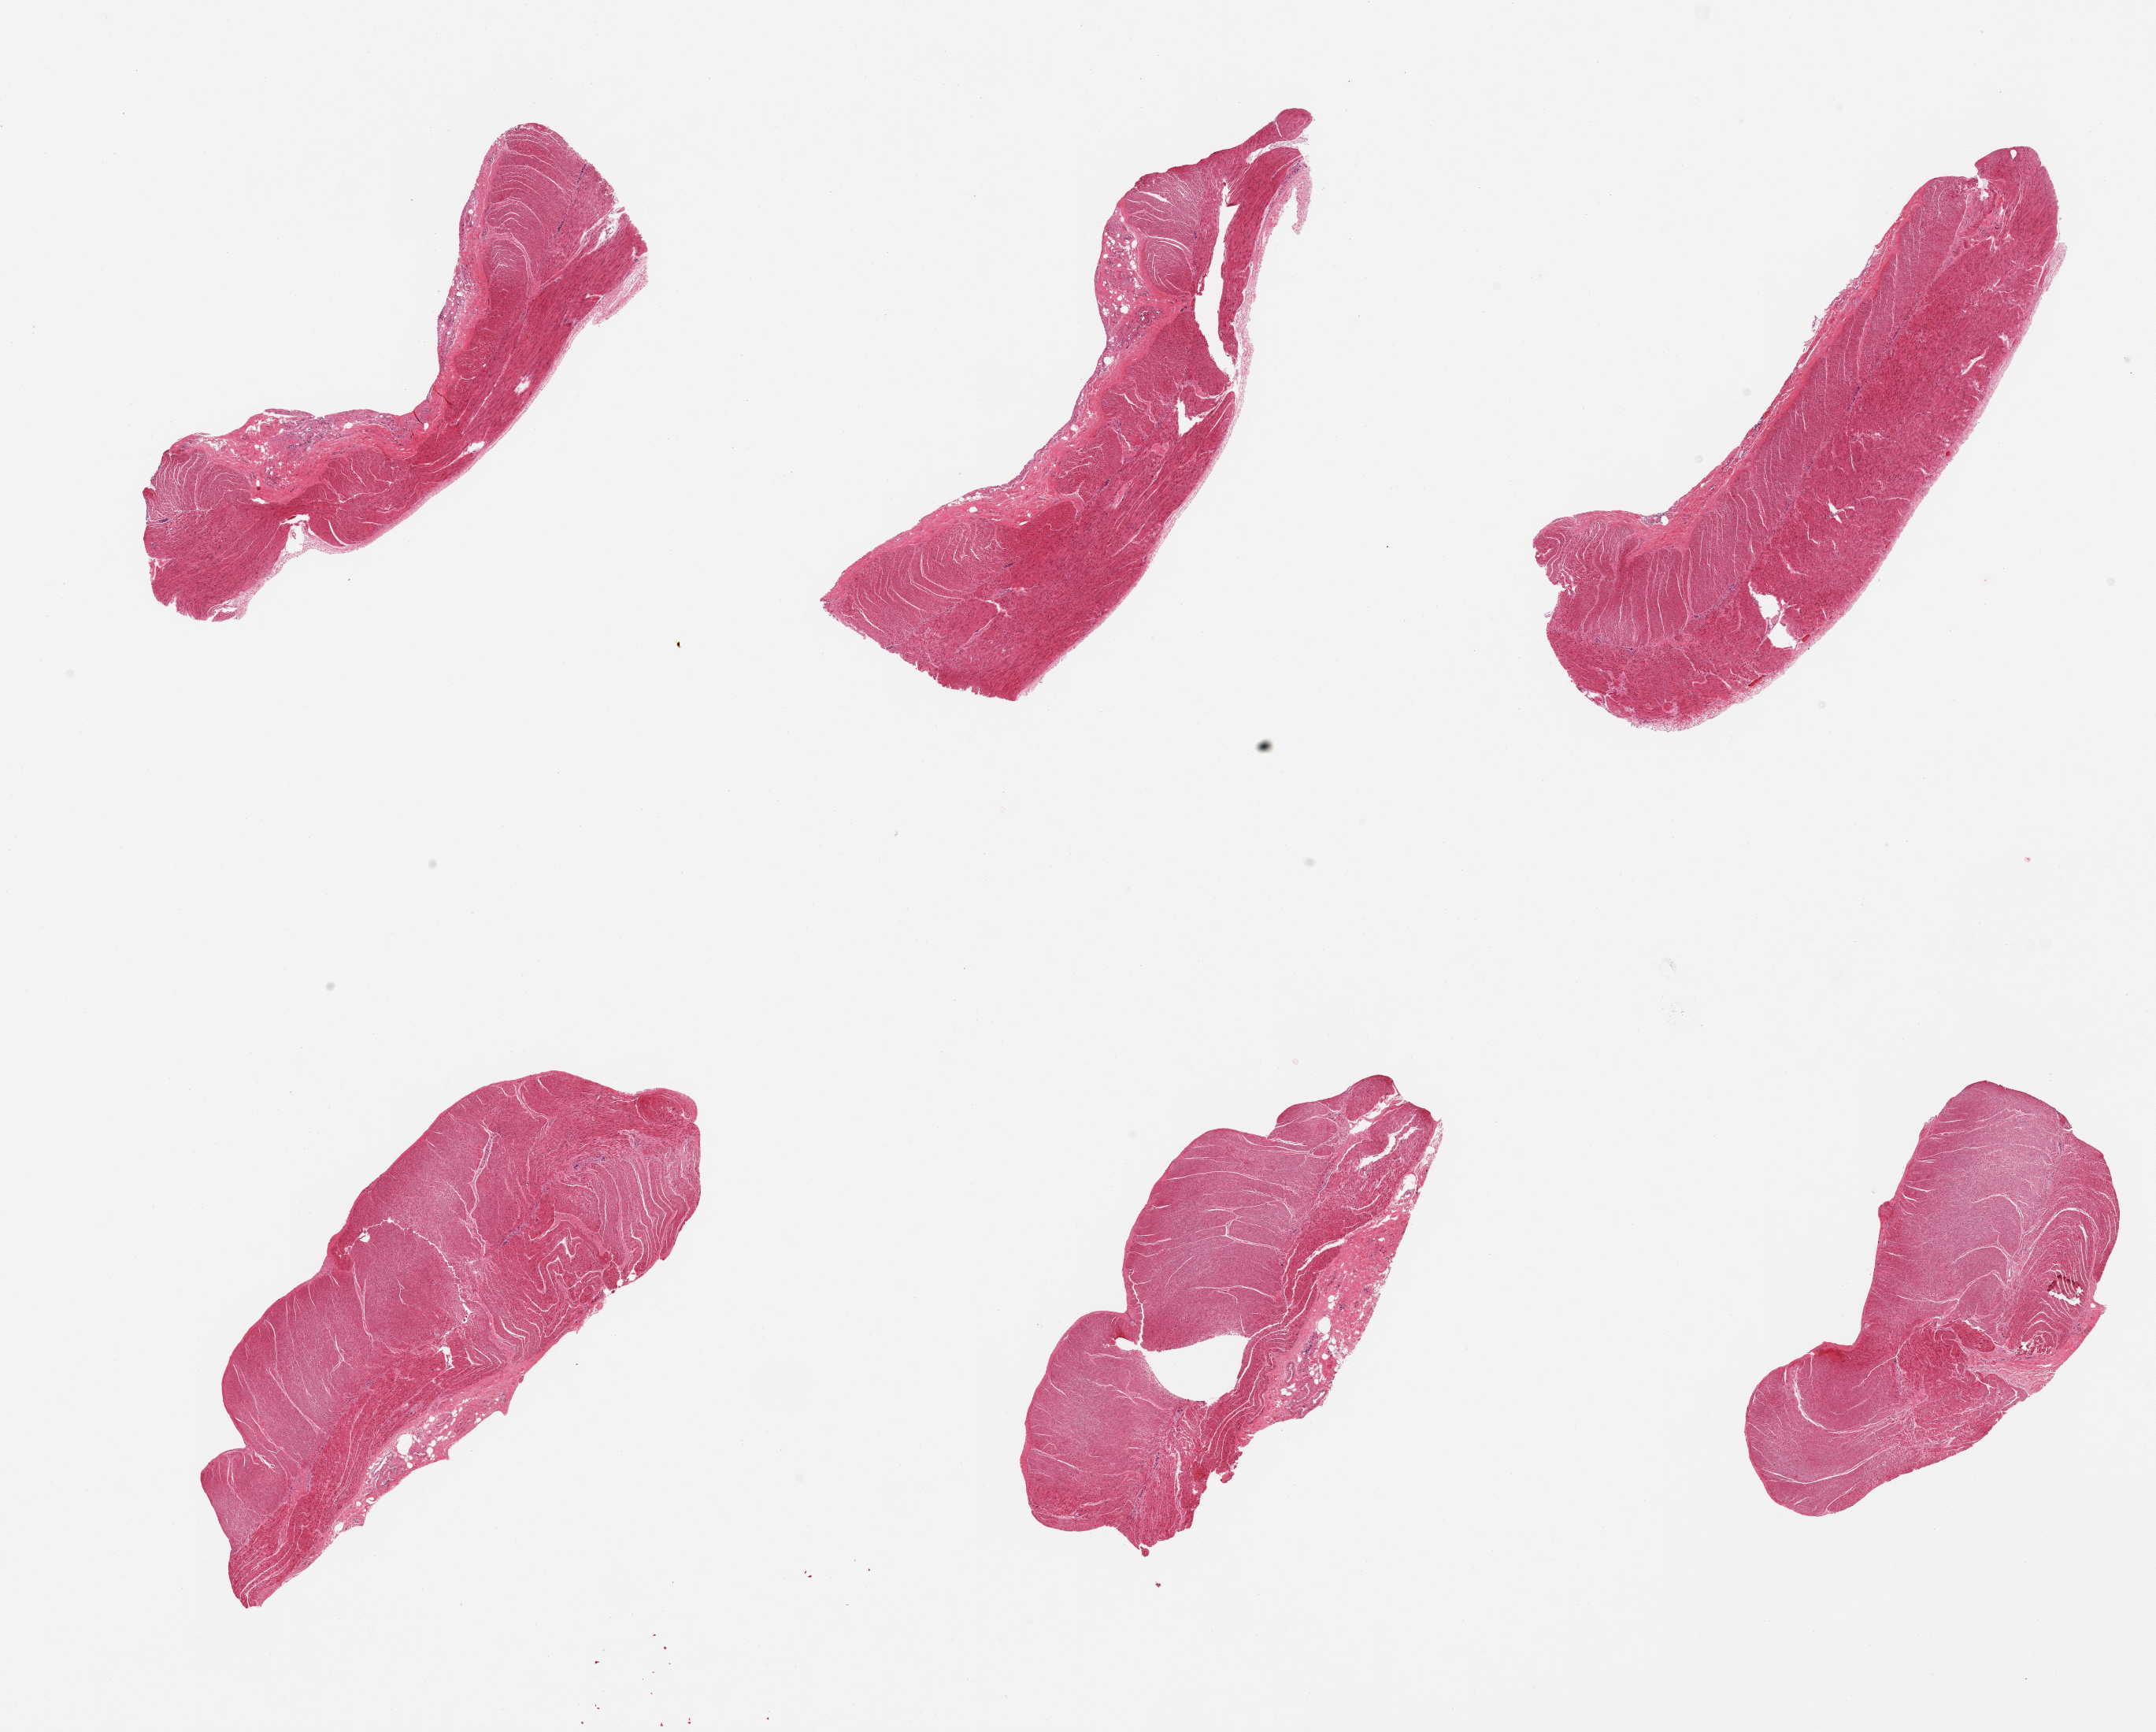
Hematoxylin and eosin (H&E) whole-slide image, low-resolution overview of the scanned area, about 21.7 x 17.4 mm (from a 20x scan); PAXgene-fixed, paraffin-embedded tissue; sampled site (target tissue): sigmoid colon; donor tissue sample. Donor: male.
Reviewer comment on this tissue sample: 6 pieces; well trimmed.